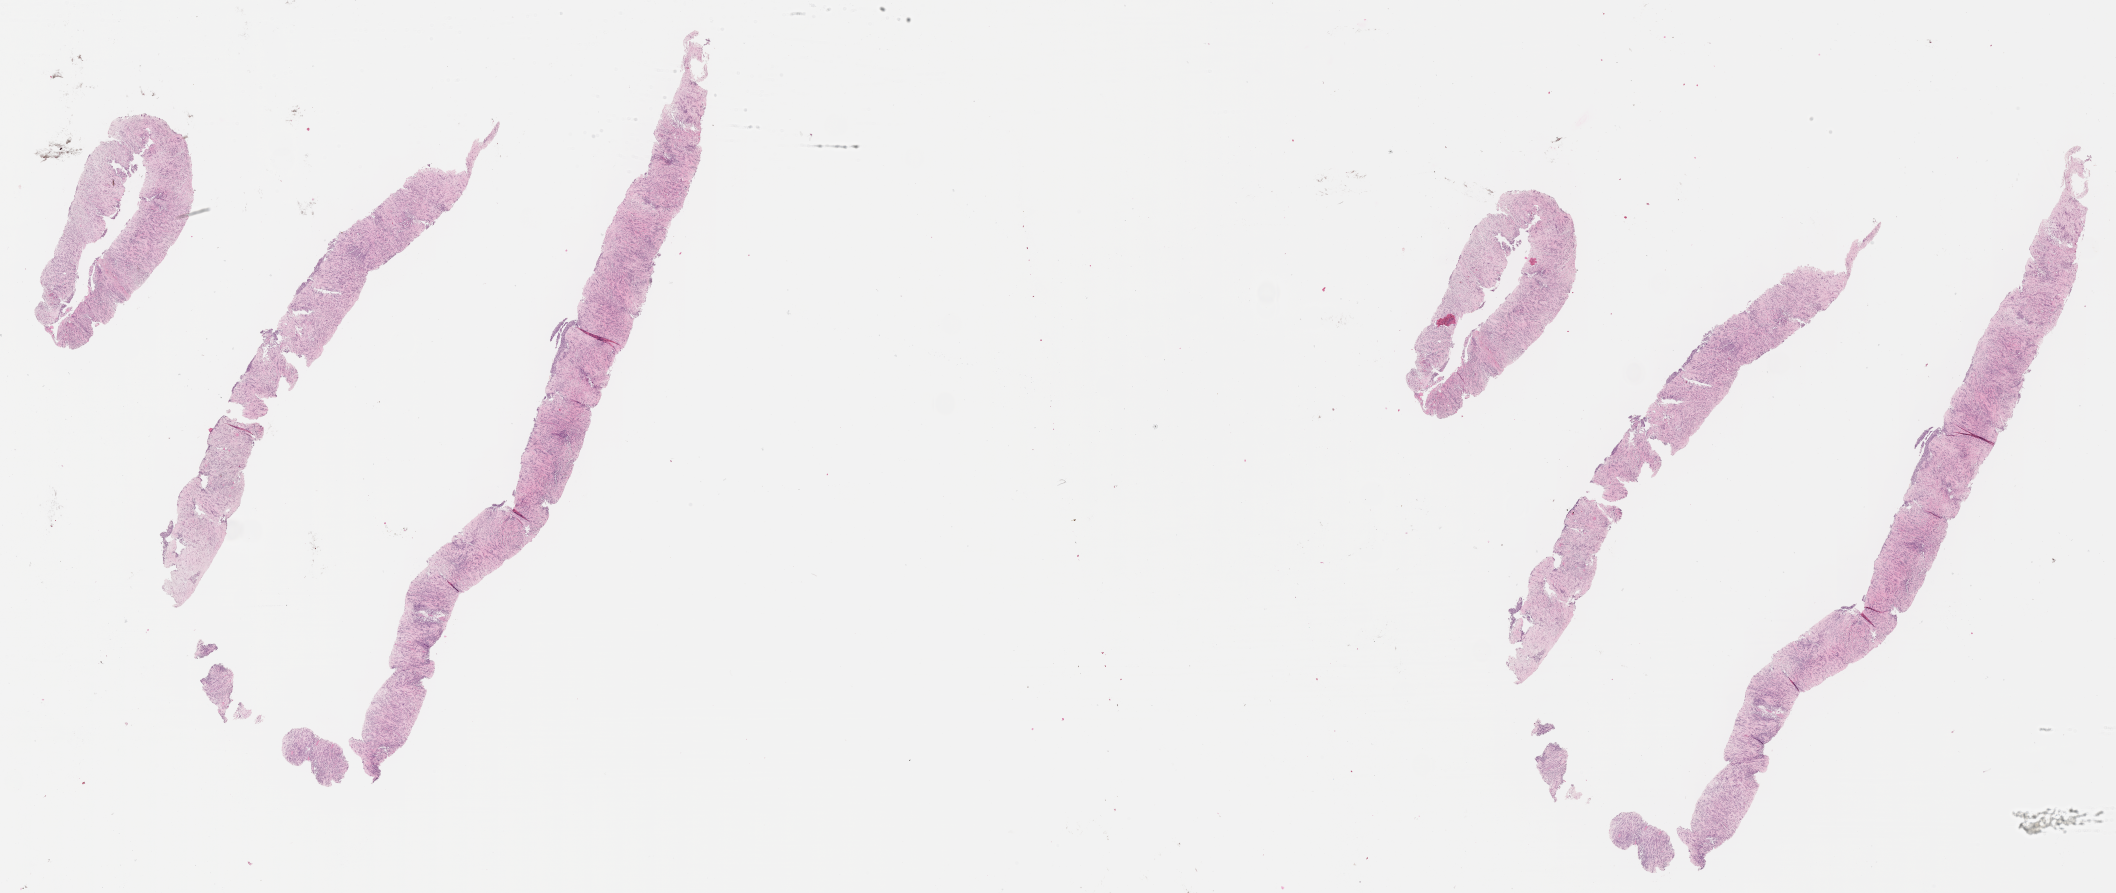
Haematoxylin and eosin whole-slide image of tumor tissue — a low-resolution overview of the entire scanned area, about 34.2 x 14.4 mm; FFPE section; site: pharynx-left. Male patient, age at diagnosis 21.1 years.
Diagnosis: rhabdomyosarcoma; histological classification: embryonal rhabdomyosarcoma. Metastatic status at presentation (as recorded): non-metastatic. Primary site (case record): parapharyngeal Area. Stage (as recorded): 3.